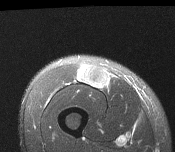
MRI of an extremity soft-tissue mass, one axial slice. Position 47 of 116 along the scan axis. T2-weighted fat-saturated. MR volume resampled by the dataset authors to the PET/CT grid (not the native acquisition matrix). 3.27 mm slice thickness. 175 × 152 image matrix, field of view 171 × 148 mm. Male patient. Case-level facts recorded for this patient, not image findings: histological type: pleiomorphic leiomyosarcoma; grade: intermediate; site of the primary tumour: right thigh.
Structures marked on this image (expert contour drawn on MRI and transferred to this co-registered scan by the dataset authors):
- gross tumour volume including surrounding oedema: bounding box (x1, y1, x2, y2) in pixels: (77, 65, 110, 89)